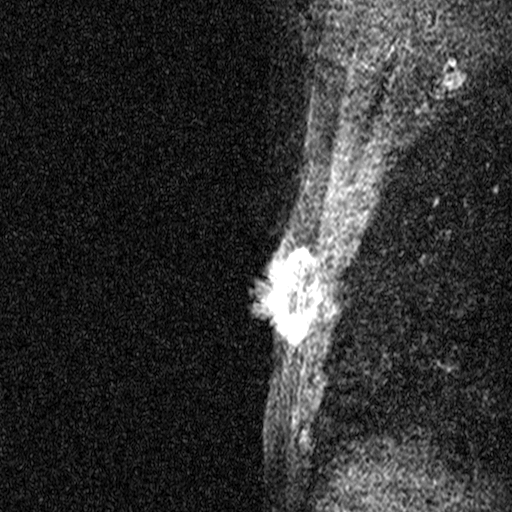
Breast MRI (dynamic contrast-enhanced), one sagittal slice; dynamic contrast-enhanced study with each time point stored as its own series, time point 2 of 3 at this slice position (early post-contrast, ordered by acquisition time); 1.5 T; TE 4.5 ms, TR 11 ms; 3 mm slice thickness; 512 × 512 image matrix, field of view 200 × 200 mm. Female patient, age 45 years. Case-level facts recorded for this patient, not image findings: setting: breast cancer imaged before/during neoadjuvant chemotherapy; receptor status: HR-positive, HER2-negative.
Outlined on this slice (semi-automatic segmentation, software-assisted and operator-edited):
- analysis volume of interest (the breast-tissue region the enhancement analysis was run in; not a lesion): bounding box [x1, y1, x2, y2] px = [256, 218, 323, 359]
- tumour enhancement mask (voxels above the 90 % enhancement threshold inside the analysis volume of interest): [268, 249, 308, 325]